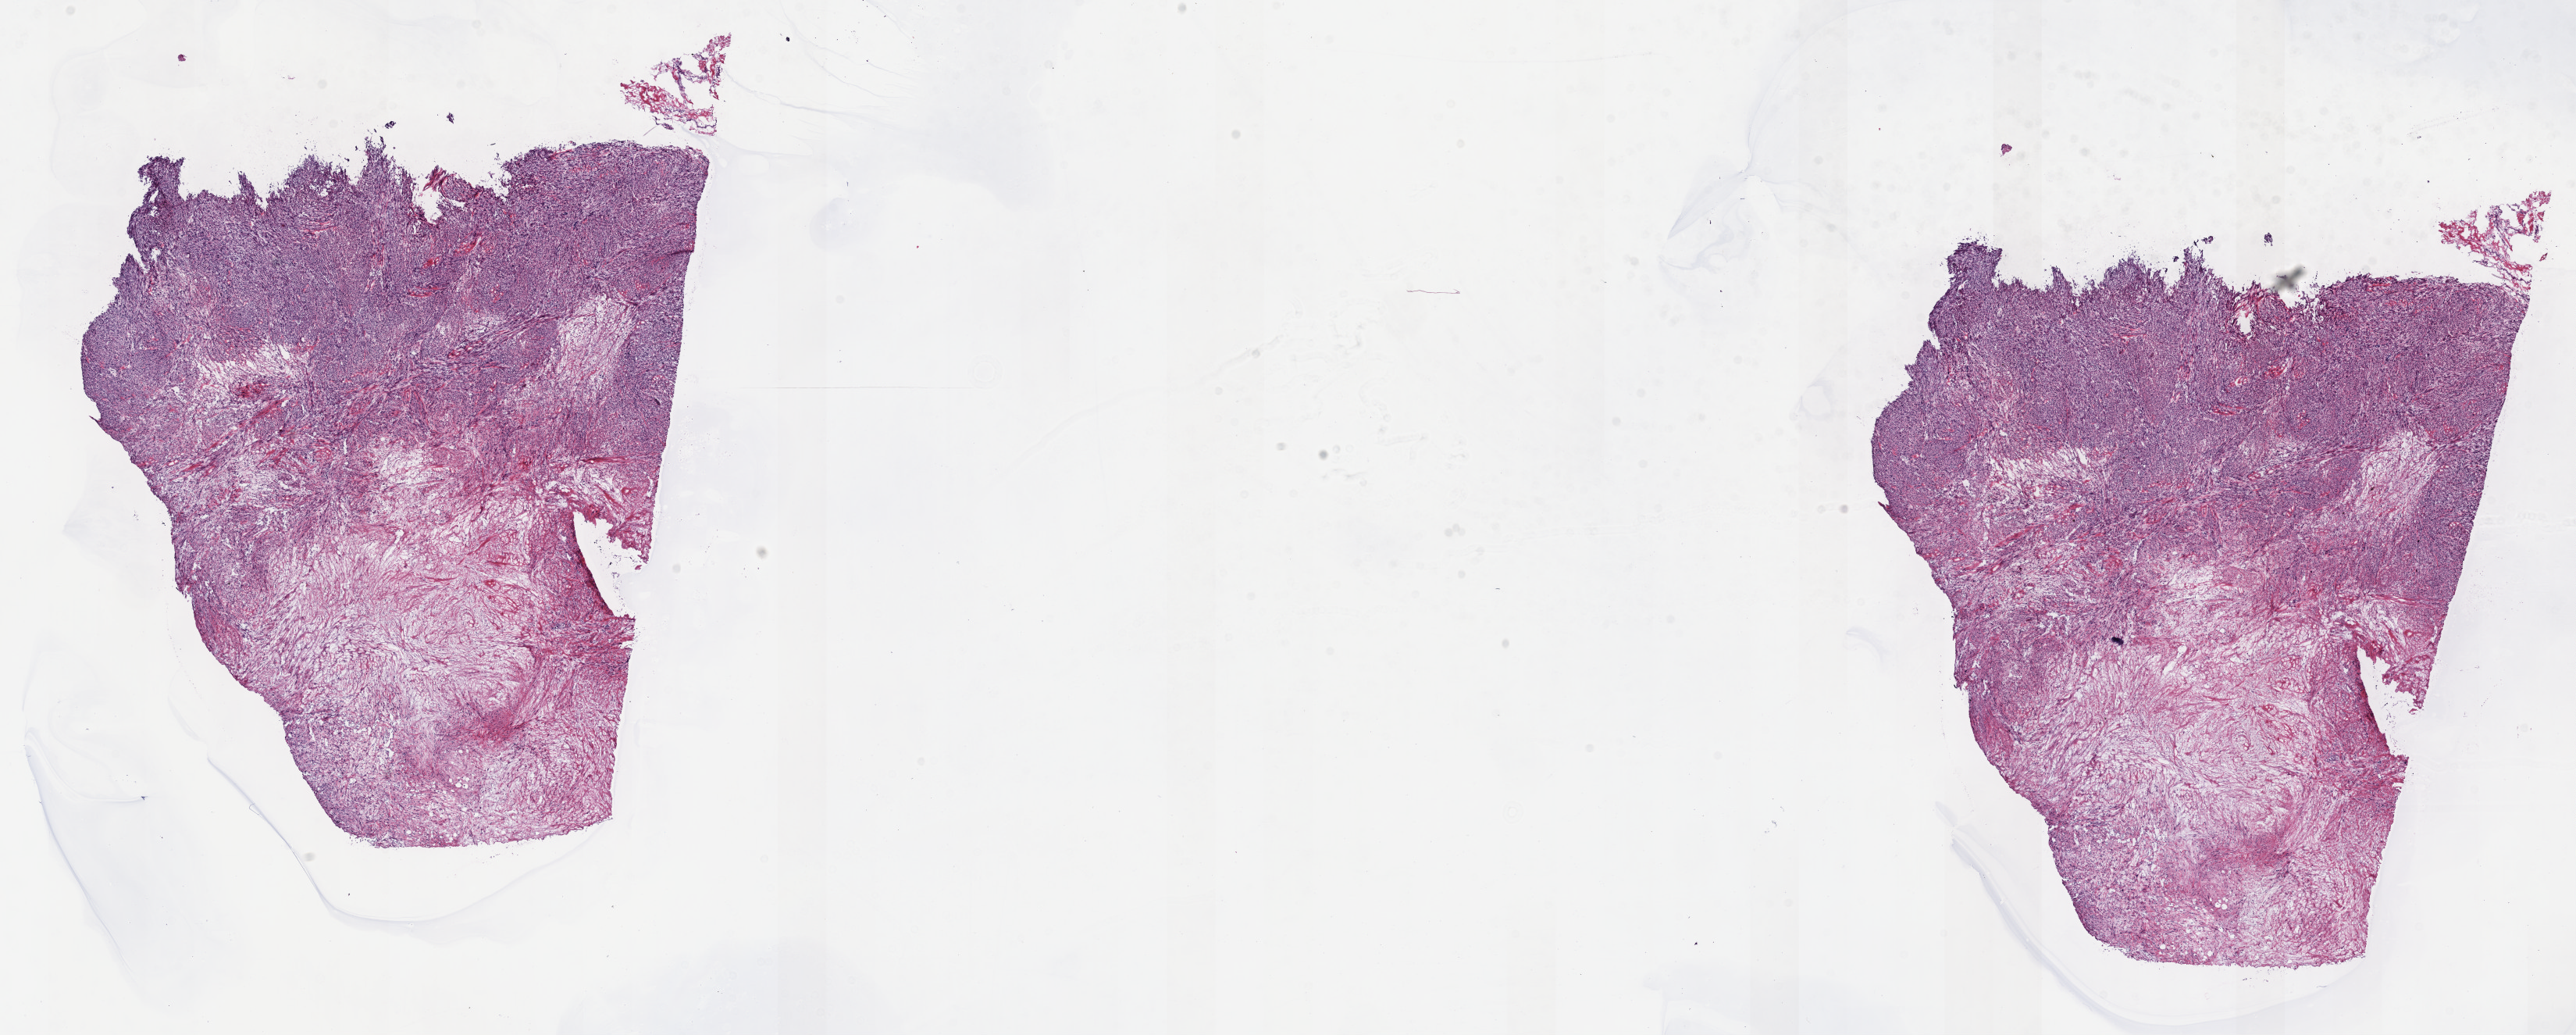
Digitized H&E-stained tissue section (whole slide) — whole scanned area (about 26.7 x 10.7 mm) shown as a low-resolution overview. Frozen section from the top of the tissue portion. Connective, subcutaneous and other soft tissues, primary tumour sample. Female, age 52 years at initial diagnosis. Slide review estimates, as recorded: tumour cells 40%, tumour nuclei 100%, normal cells 0%, stromal cells 40%, necrosis 20%. Inflammatory infiltration, as recorded: lymphocyte infiltration 0%, monocyte infiltration 0%, neutrophil infiltration 0%.
Histologic diagnosis: Leiomyosarcoma, NOS.